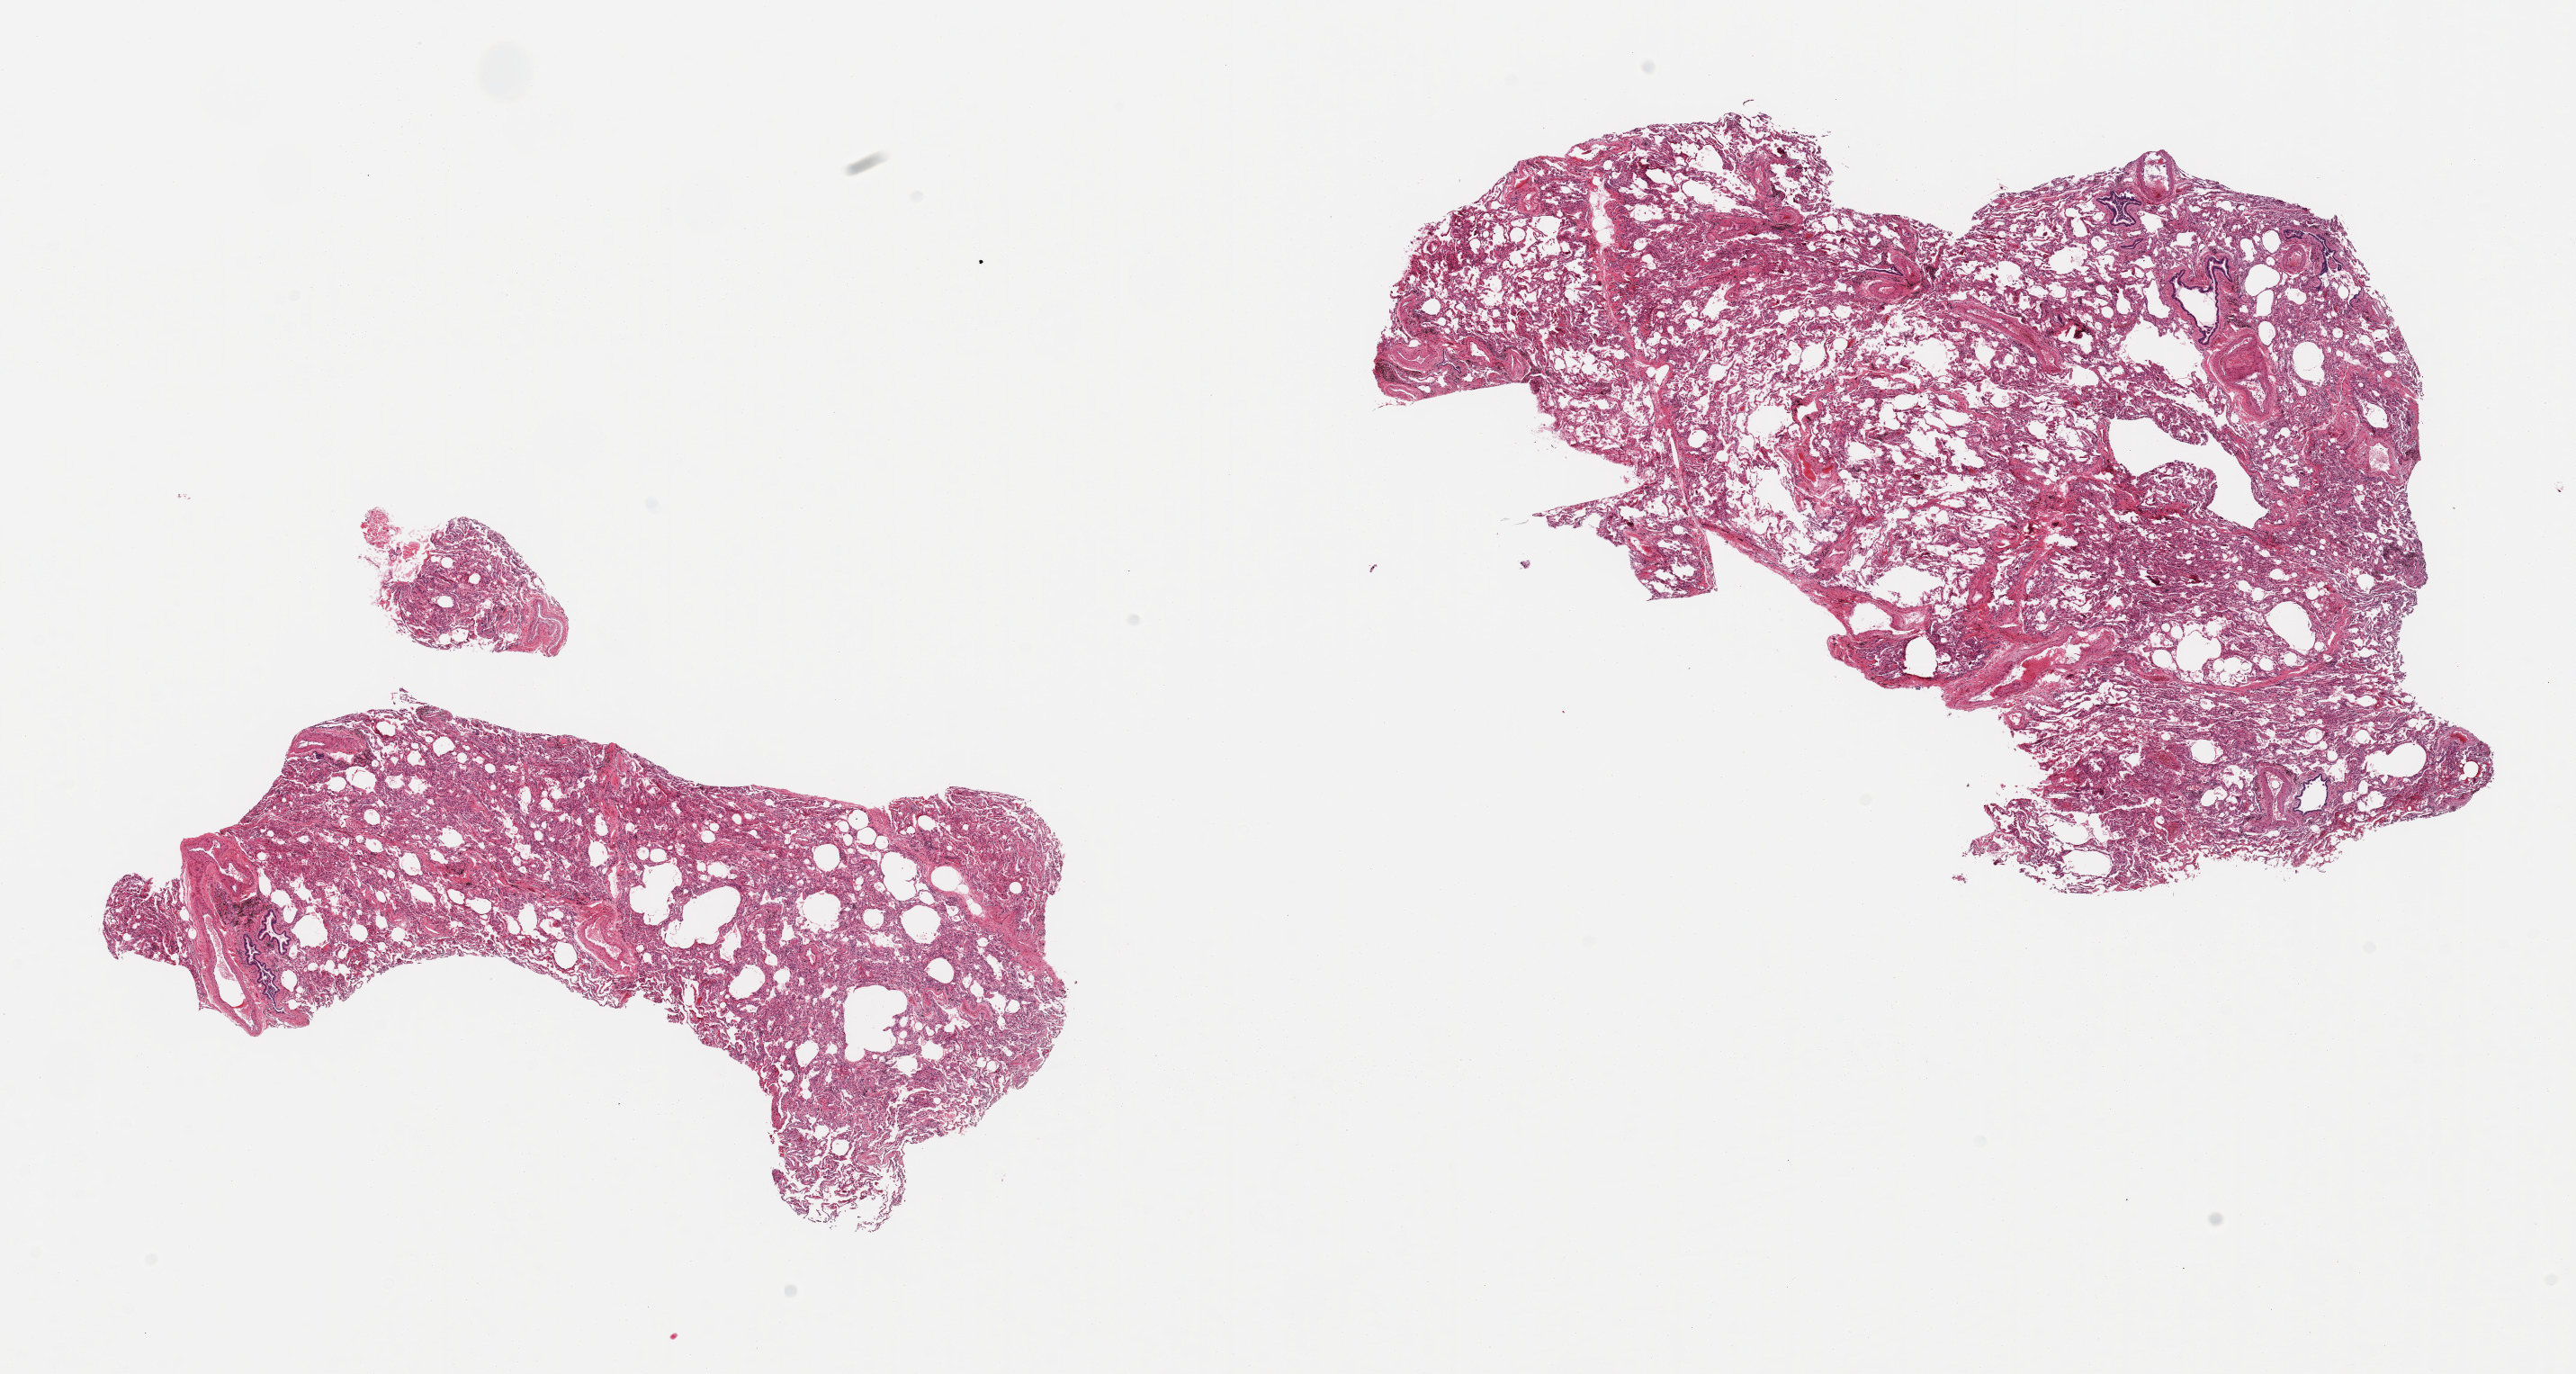
Whole-slide image, hematoxylin and eosin (H&E) stain, whole scanned area (about 22.6 x 12.1 mm, from a 20x scan) shown as a low-resolution overview; PAXgene-fixed, paraffin-embedded tissue; section of lung (target tissue); tissue donor sample. Male donor.
Reviewer comment on this tissue sample: 2 pieces, mild congestion.